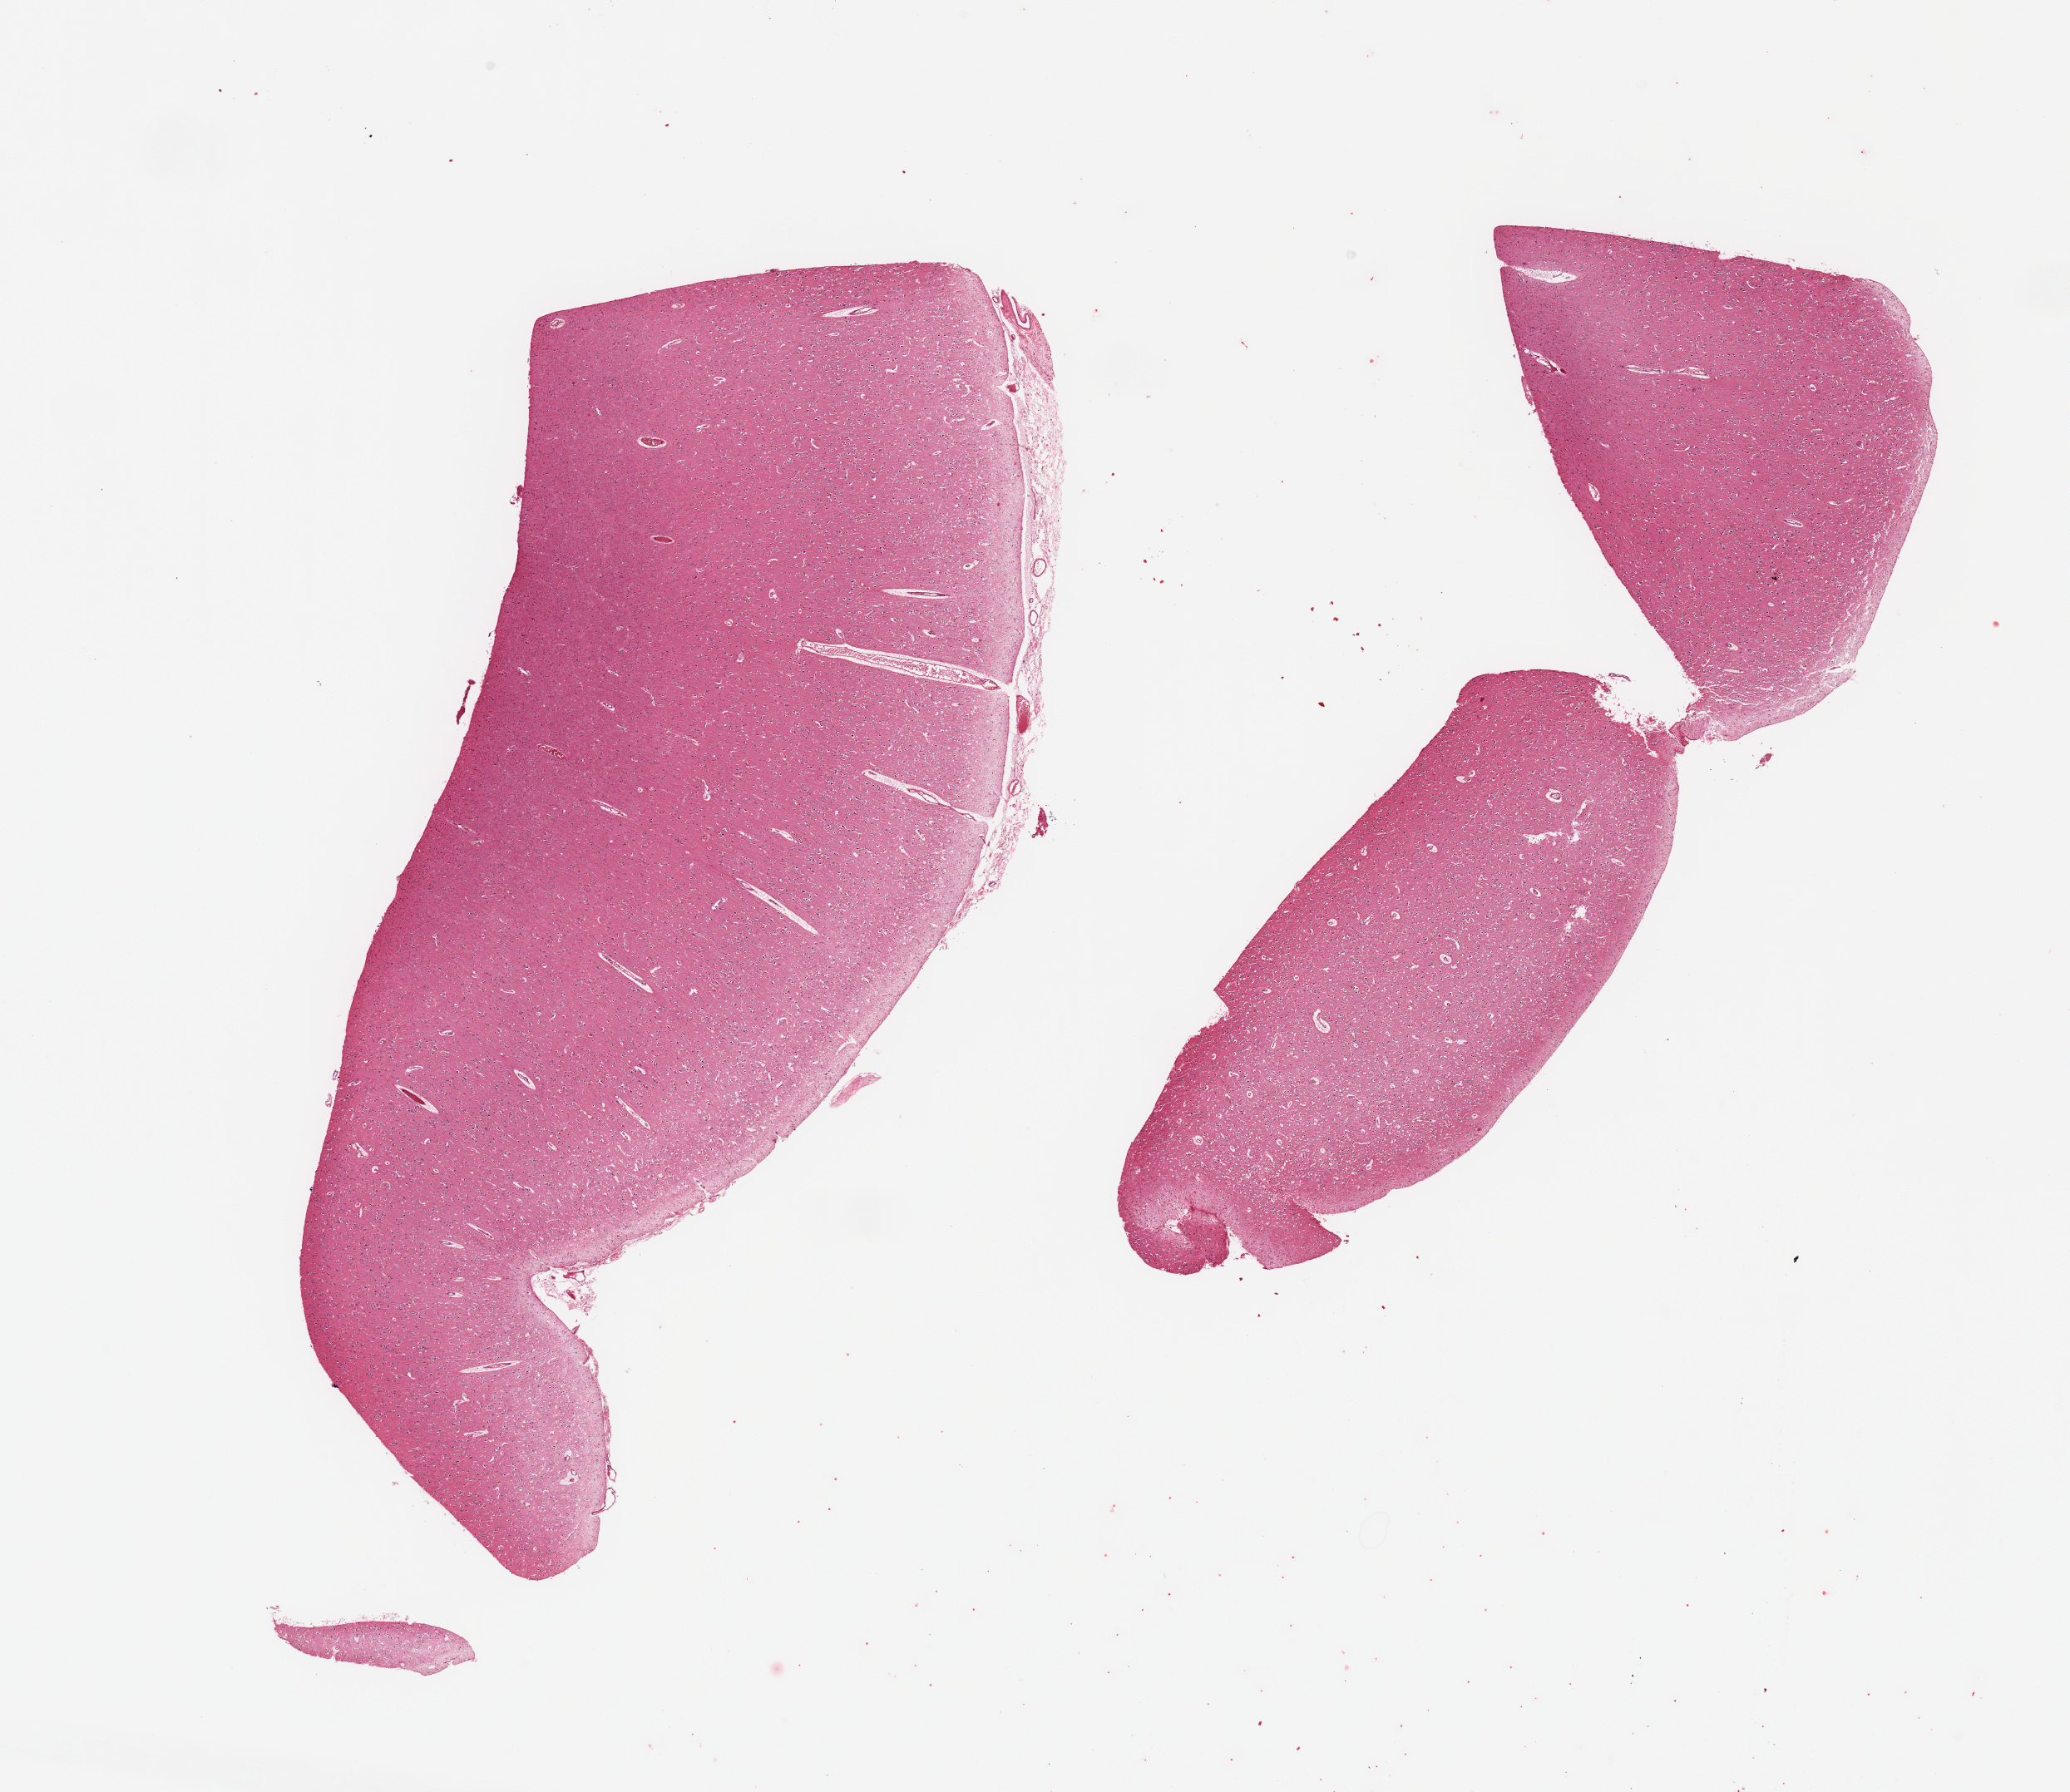
Digitized haematoxylin and eosin-stained section — a low-resolution overview of the entire scanned area, about 19.7 x 17.0 mm, PAXgene-fixed paraffin-embedded (PFPE) section, sampled site (target tissue): cerebral cortex, donor tissue sample. Donor: male.
- reviewer comment on this tissue sample: 2 pieces, no abnormalities